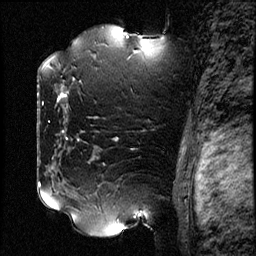
Breast MRI (dynamic contrast-enhanced), one sagittal slice; slice 57 of 78 in the series (ordered by position); dynamic contrast-enhanced study with each time point stored as its own series, time point 2 of 3 at this slice position (early post-contrast, ordered by acquisition time); 1.5 T; TE 4.2 ms, TR 17.6 ms; 2 mm slice thickness; 256 × 256 image matrix, field of view 200 × 200 mm. Female patient, age 42 years. From the clinical record (not read from this slice): setting: breast cancer imaged before/during neoadjuvant chemotherapy; receptor status: HER2-positive.
Outlined on this slice (semi-automatic segmentation, software-assisted and operator-edited):
- analysis volume of interest (the breast-tissue region the enhancement analysis was run in; not a lesion): bounding box <50,48,131,129> (left, top, right, bottom; pixels)
- tumour enhancement mask (voxels above the 100 % enhancement threshold inside the analysis volume of interest): <60,92,67,98>